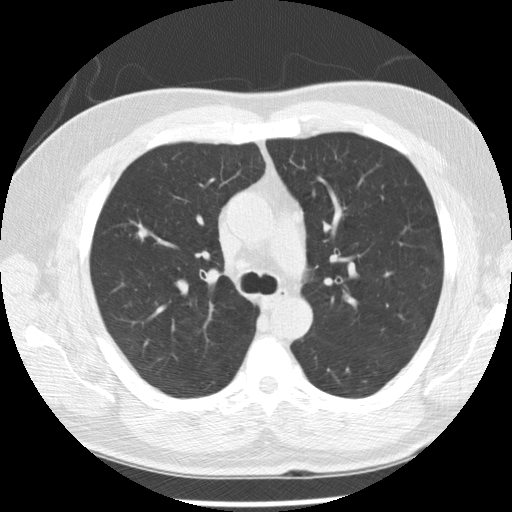
Low-dose screening chest CT, axial slice; first (baseline) screen; lung window (W 1500 / L -600 HU); 2.5 mm slice thickness; slice 88 of 265 in the series. Male participant, aged 57 years at enrolment. Former smoker at enrolment.
Lesion marked by an expert reader, bounding box [x1, y1, x2, y2] px = [125, 221, 158, 253]. Reader record for this screening exam (exam-level; its link to the box is not recorded): non-calcified nodule or mass ≥4 mm, right upper lobe, 7 × 7 mm, poorly defined margins, soft tissue attenuation. Lung cancer was diagnosed 125 days after this screen: squamous cell carcinoma, NOS, right upper lobe, moderately differentiated (G2), stage IA (AJCC 6th edition), 10 mm at pathology.